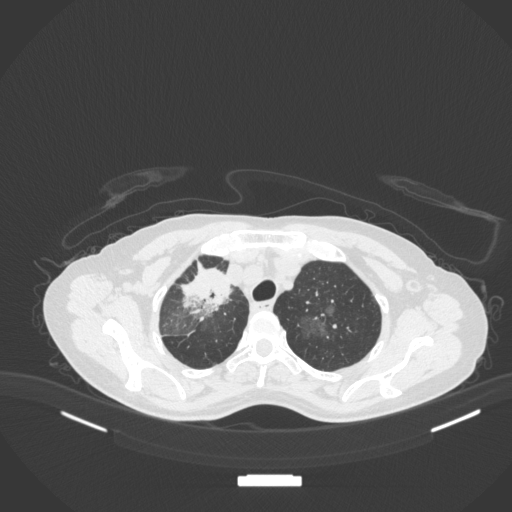
Chest CT, one axial slice. Position 267 of 311 along the scan axis. 120 kVp. Lung window (W 1500 / L -600 HU). 1 mm slice thickness. 512 × 512 image matrix, field of view 400 × 400 mm. Patient: female, 59 years. Case-level facts recorded for this patient, not image findings: clinical TNM (as recorded): T3 N0 M0; histopathological grade: G1.
Structures marked on this image (rectangle marked by the reading radiologist):
- lung tumour (recorded histology: adenocarcinoma): box from (x=171, y=255) to (x=240, y=321) px